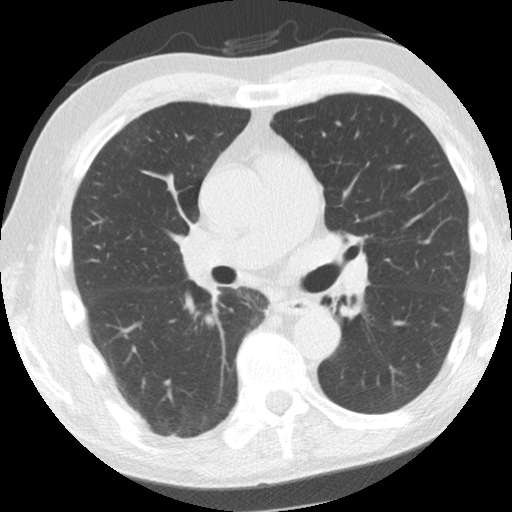
Chest CT (low-dose screening protocol), one axial image, second annual screen, lung window (W 1500 / L -600 HU), 512 × 512 image matrix, field of view 324 × 324 mm. Male participant, aged 61 years at enrolment. Former smoker at enrolment.
• Expert reader's lesion annotation, box from (x=302, y=288) to (x=348, y=325) px.
• Screening reader's record for this exam: no non-calcified nodule ≥4 mm recorded.
• Official screen result: negative screen, minor abnormalities not suspicious for lung cancer.
• Participant outcome: lung cancer diagnosed 775 days after this screen (after the third annual screen) — squamous cell carcinoma, NOS, left upper lobe, left lower lobe, well differentiated (G1), stage IIB (AJCC 6th edition), 100 mm at pathology.